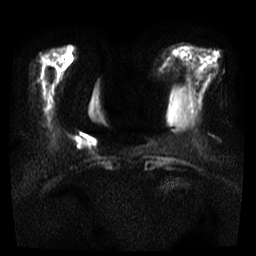
Breast MRI, one axial slice; slice 10 of 35 in the series (ordered by position); diffusion-weighted series; image 2 of 4 stored at this slice position (different b-values; order by instance number); 3 T; 5 mm slice thickness; 256 × 256 image matrix. Female patient.
Structures marked on this image (expert manual segmentation):
- tumour on diffusion-weighted imaging: bounding box <73,135,94,147> (left, top, right, bottom; pixels)